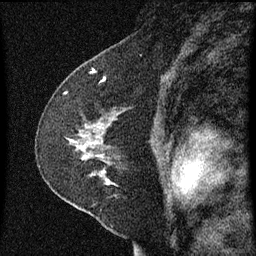
Breast MRI (dynamic contrast-enhanced), one sagittal slice; slice 41 of 60 in the series (ordered by position); dynamic contrast-enhanced series, image 2 of 3 at this slice position (ordered by acquisition); 1.5 T; TE 4.2 ms, TR 8 ms; 2 mm slice thickness; 256 × 256 image matrix, field of view 180 × 180 mm. Female patient, age 47 years.
Structures marked on this image (semi-automatic segmentation, software-assisted and operator-edited):
- analysis volume of interest (the breast-tissue region the enhancement analysis was run in; not a lesion): bounding box (x1, y1, x2, y2) in pixels: (36, 98, 158, 213)
- tumour enhancement mask (voxels above the 70 % enhancement threshold inside the analysis volume of interest): (69, 140, 110, 183)